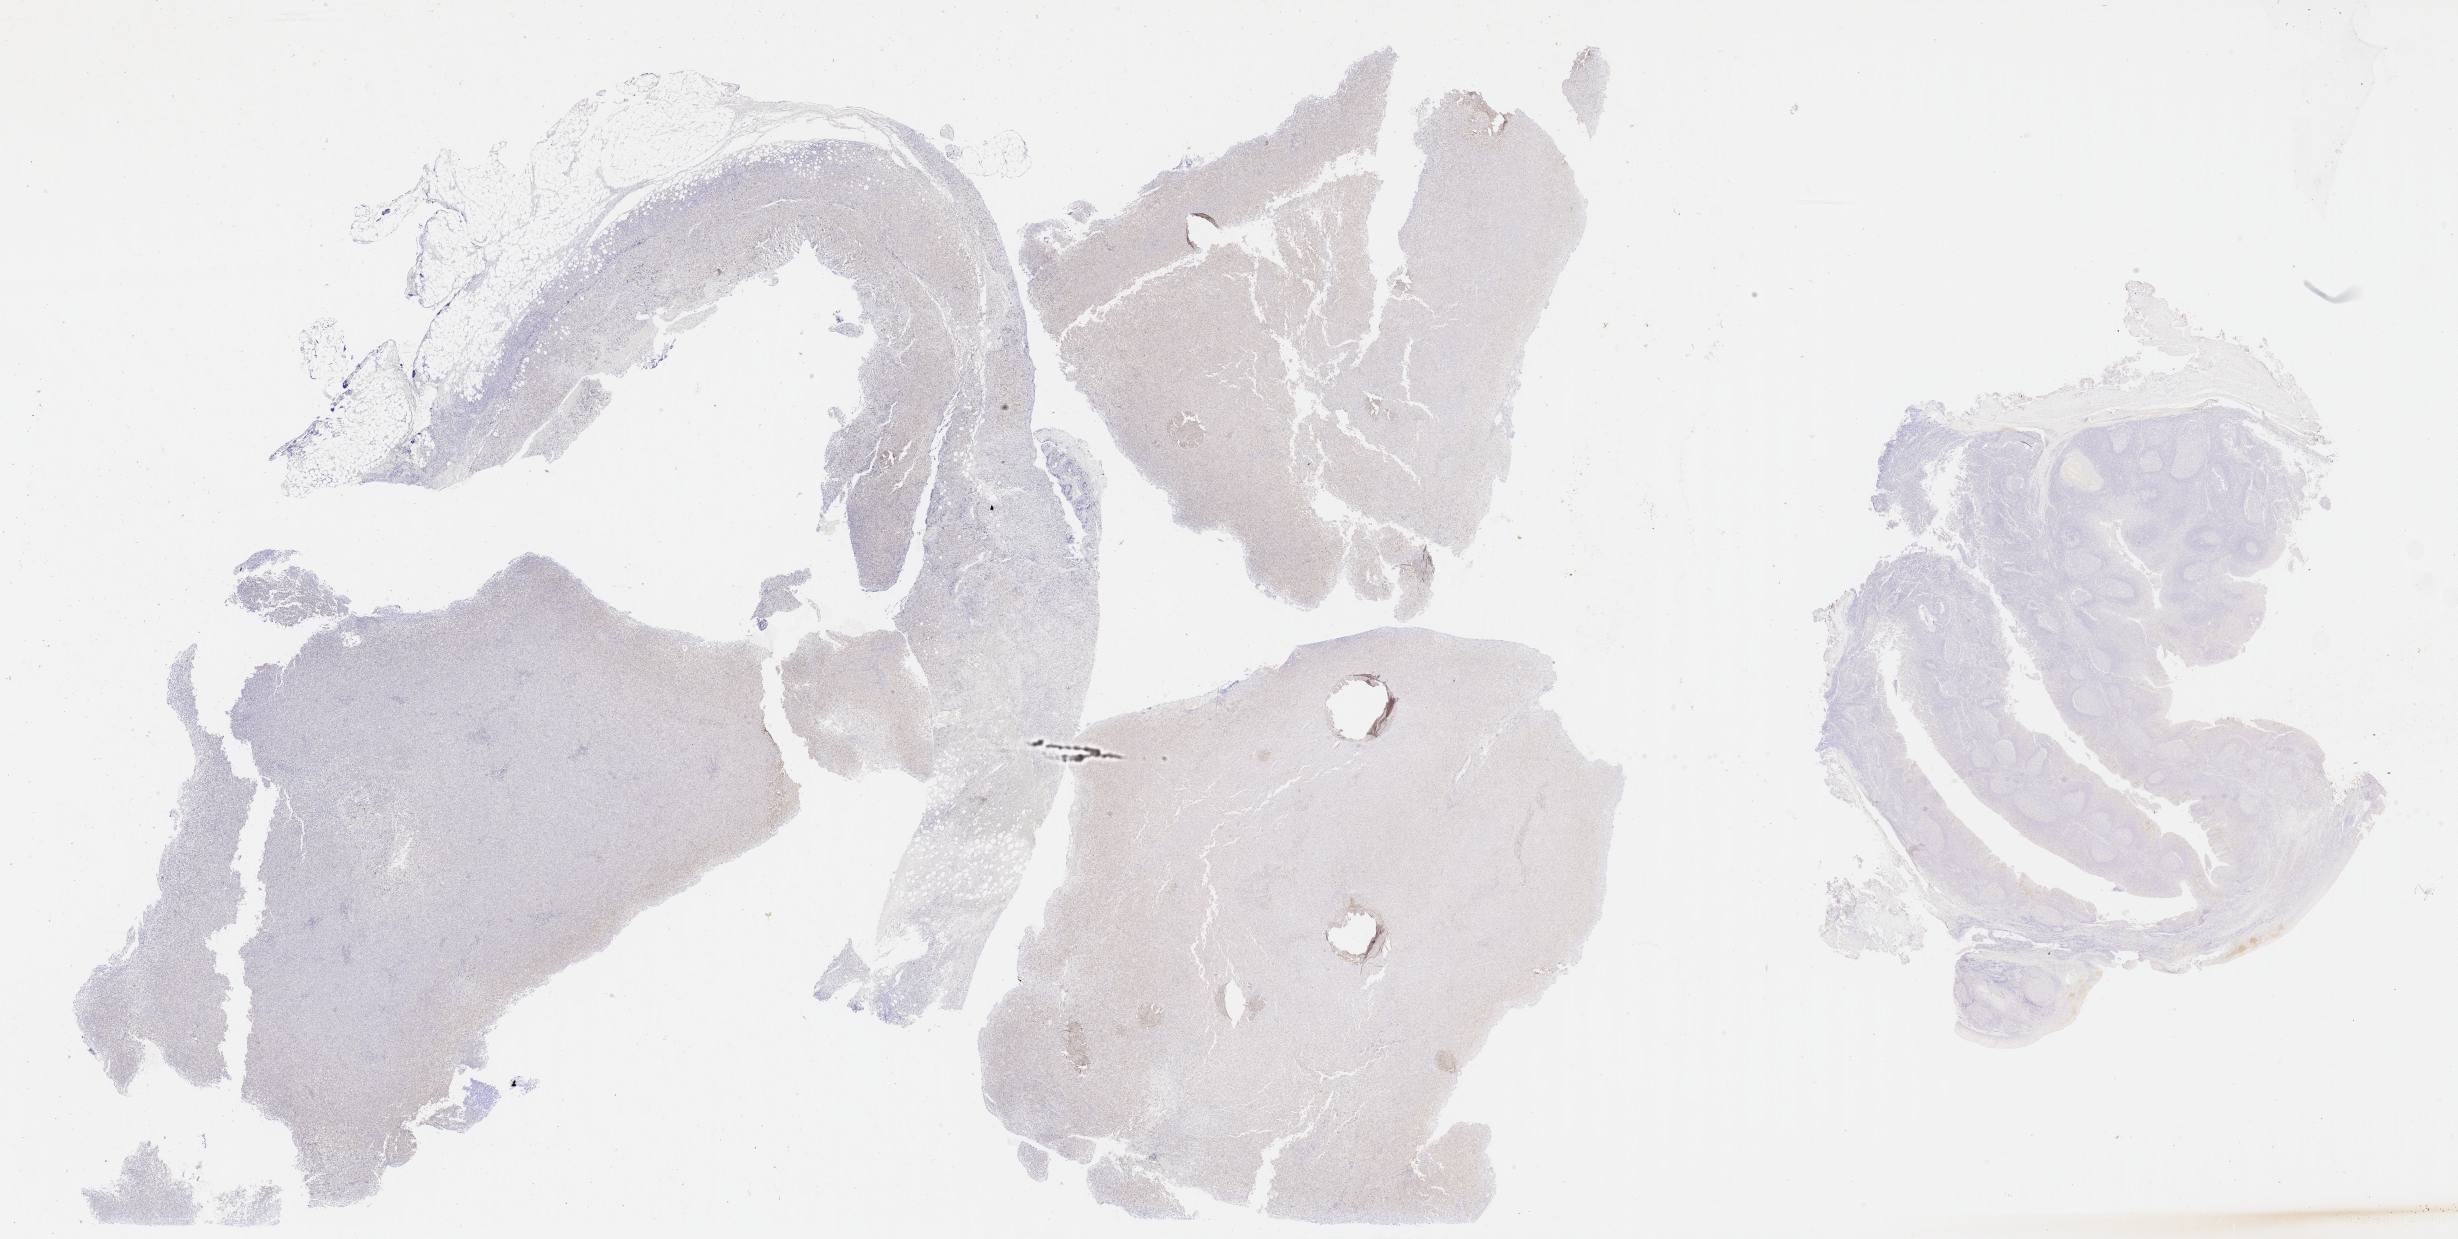
Immunohistochemistry (IHC) whole-slide image stained for IRF4/MUM1 — low-resolution overview of the scanned area, about 39.8 x 20.0 mm. Female patient.
- specimen: tumor tissue